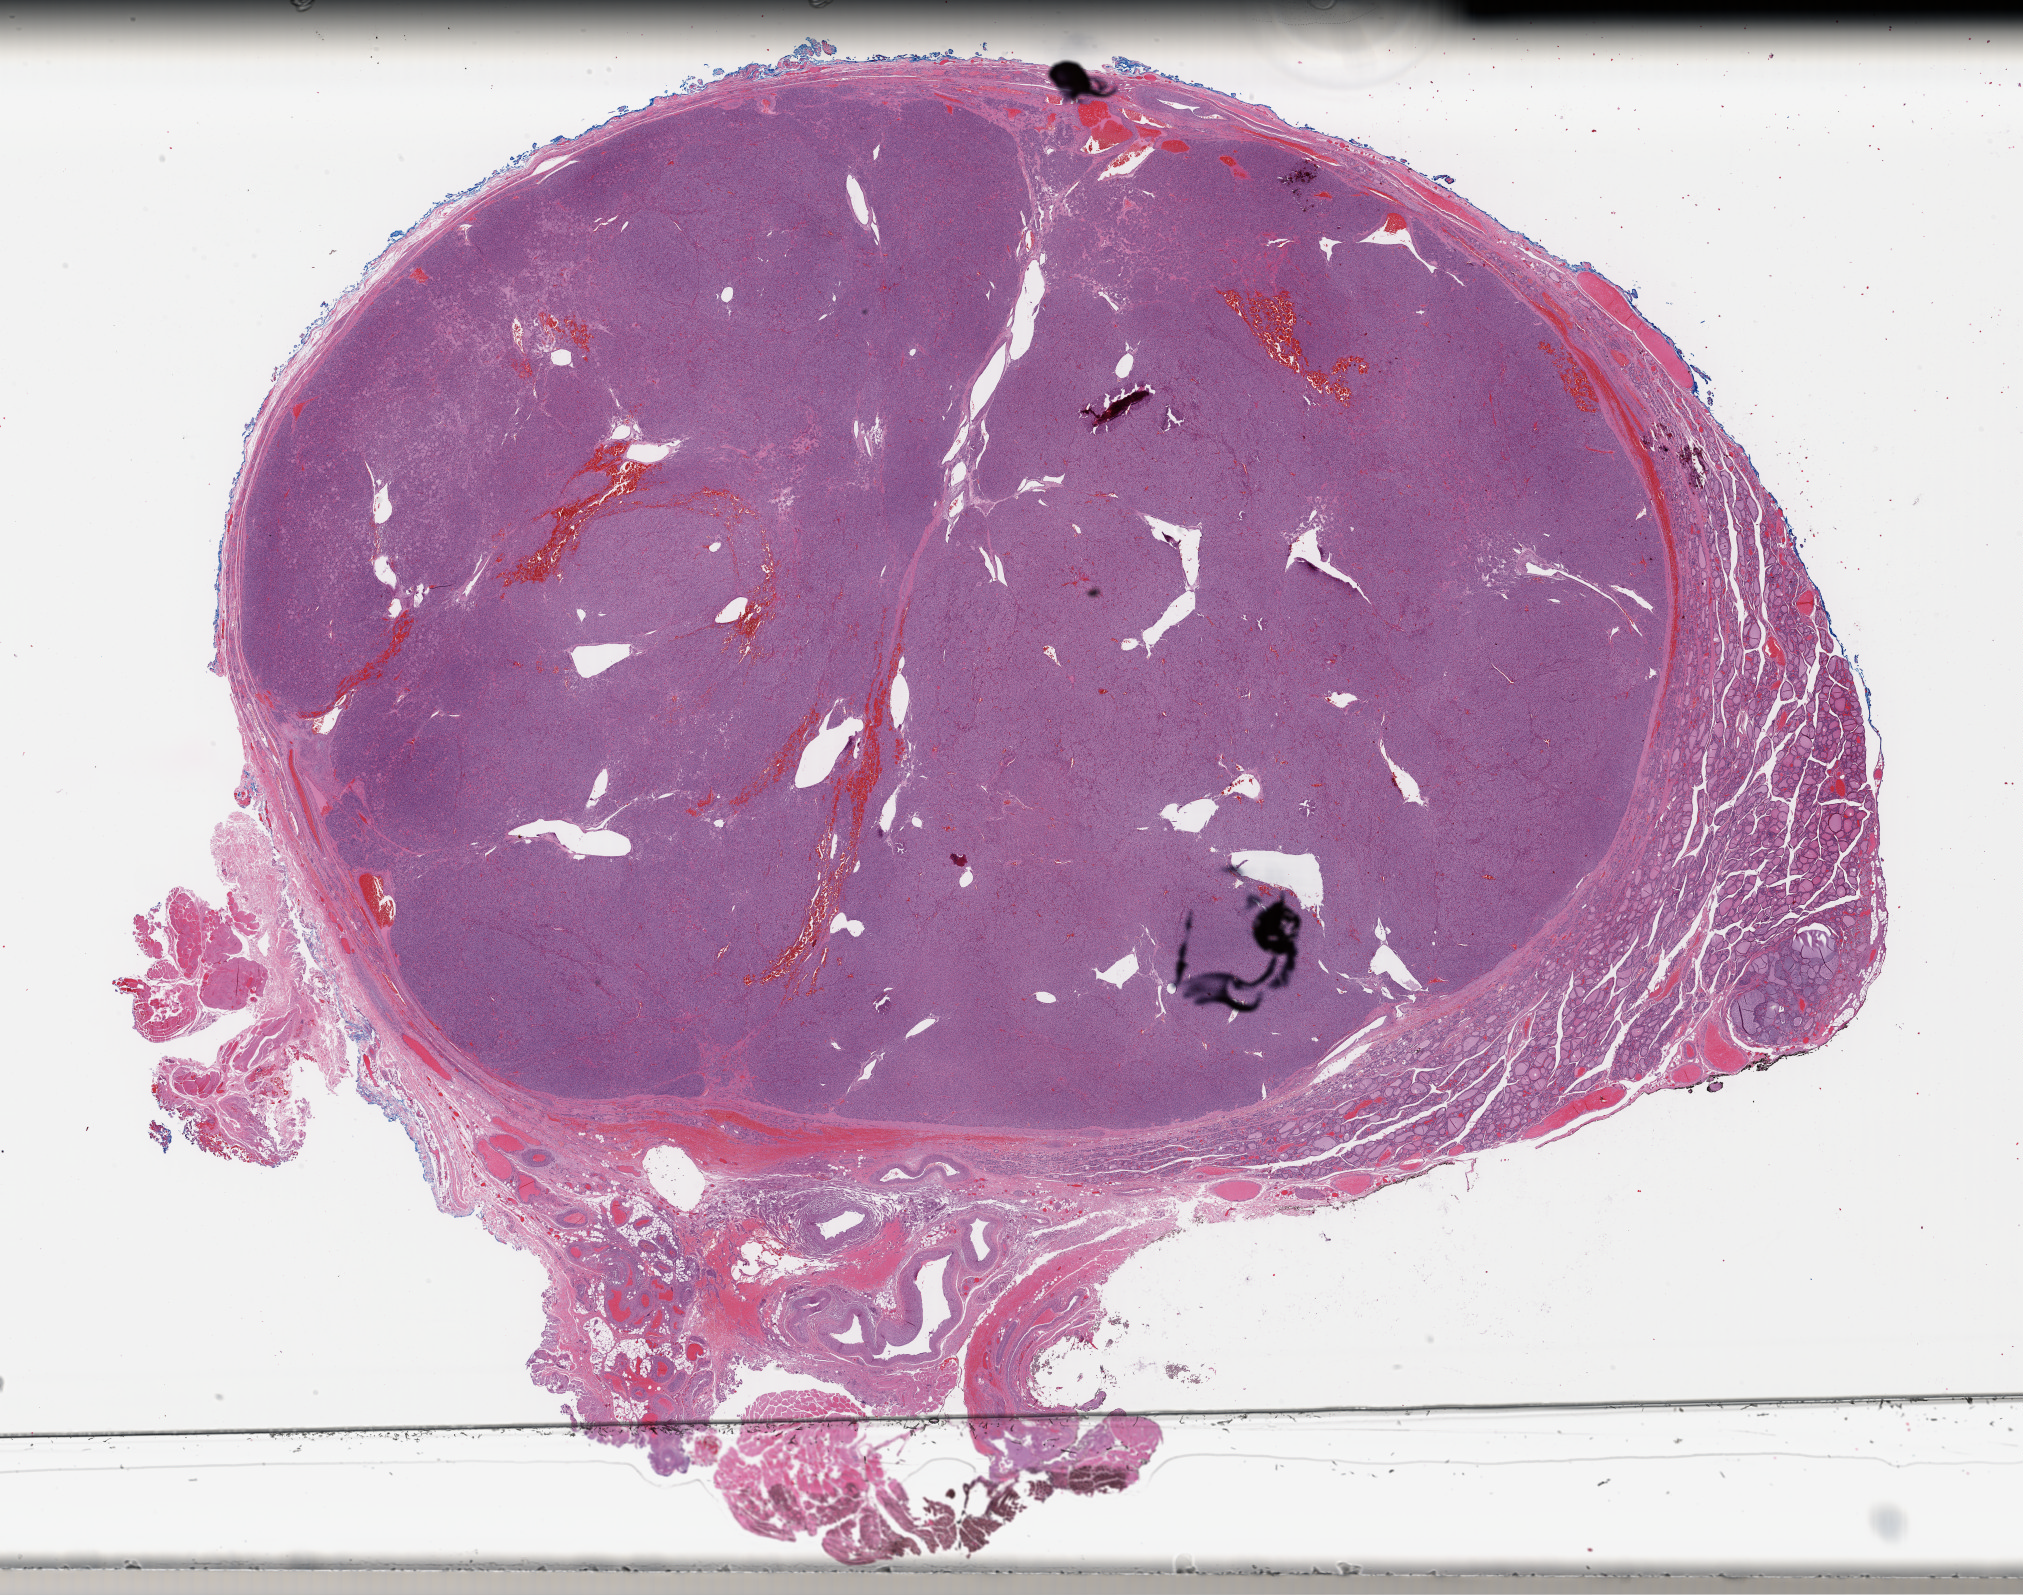
H&E whole-slide image — shown as a low-resolution overview of the whole scanned area (about 31.8 x 25.1 mm); formalin-fixed paraffin-embedded (FFPE) diagnostic section; sample: primary tumour, thyroid. Male, age 47 years at initial diagnosis.
Lymph nodes positive (case pathology): 0 of 3 examined. AJCC pathologic stage: II (7th edition). Diagnosis: Papillary carcinoma, follicular variant (thyroid gland).